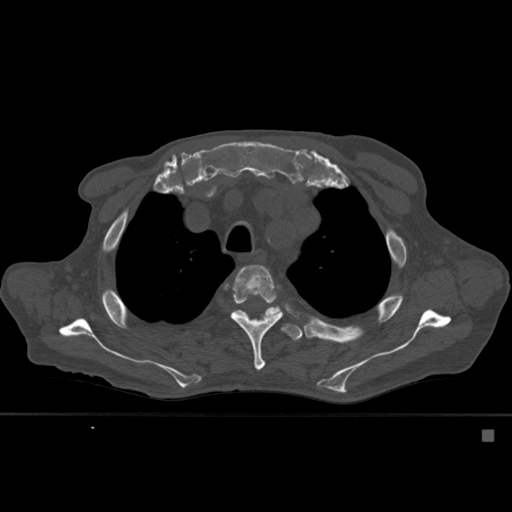
CT including the spine, one axial slice. Slice 415 of 527 in the series (ordered by position). Bone window (W 1800 / L 400 HU). 1.5 mm slice thickness. 512 × 512 image matrix, field of view 373 × 373 mm. Male patient, age 78 years. Case-level facts recorded for this patient, not image findings: primary cancer: prostate.
Structures marked on this image (semi-automatically segmented with operator editing):
- T4 vertebra: bounding box [x1, y1, x2, y2] px = [230, 265, 283, 371]
- T5 vertebra: [233, 307, 306, 341]